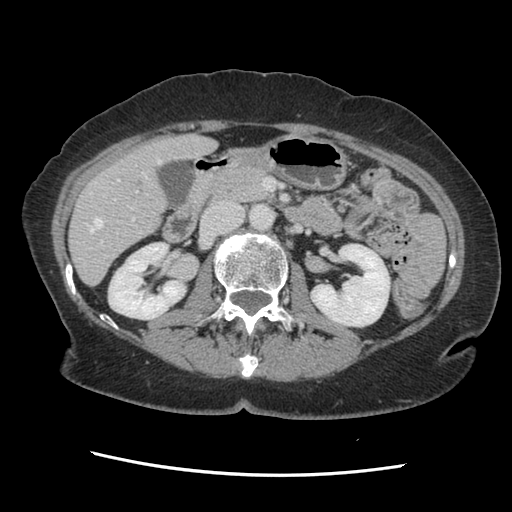
Contrast-enhanced abdominal CT, one axial slice. Slice 62 of 141 in the series (ordered by position). 120 kVp. Soft-tissue window (W 400 / L 40 HU). 2.5 mm slice thickness. 512 × 512 image matrix, field of view 330 × 330 mm. Female patient, age 61 years. Case-level facts recorded for this patient, not image findings: diagnosis: colorectal cancer liver metastases, imaged before liver resection; multiple liver metastases: no; largest metastasis: 2.4 cm.
Structures marked on this image (outlined manually by an expert reader):
- hepatic veins: bounding box <86,159,161,233> (left, top, right, bottom; pixels)
- liver: <70,136,214,284>
- planned liver remnant (the part of the liver to remain after resection): <70,138,214,284>
- portal vein (with intrahepatic branches): <101,180,138,244>
- liver metastasis: <133,178,145,189>